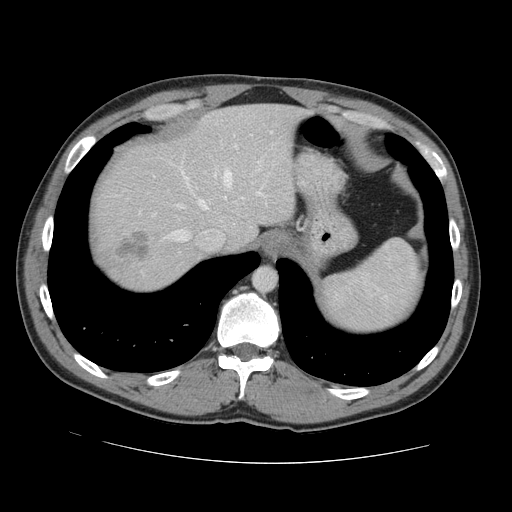
Contrast-enhanced abdominal CT, one axial slice; position 114 of 131 along the scan axis; intravenous contrast given; soft-tissue window (W 400 / L 40 HU); 2.5 mm slice thickness; 512 × 512 image matrix. Male patient, age 40 years. Case-level facts recorded for this patient, not image findings: diagnosis: colorectal cancer liver metastases, imaged before liver resection; multiple liver metastases: yes; largest metastasis: 2.9 cm; disease in both lobes: yes.
Structures marked on this image (manually delineated by an expert):
- hepatic veins: bounding box [x1, y1, x2, y2] px = [172, 170, 232, 241]
- liver: [92, 105, 301, 289]
- planned liver remnant (the part of the liver to remain after resection): [110, 105, 301, 249]
- portal vein (with intrahepatic branches): [214, 145, 263, 195]
- liver metastasis: [114, 233, 151, 262]